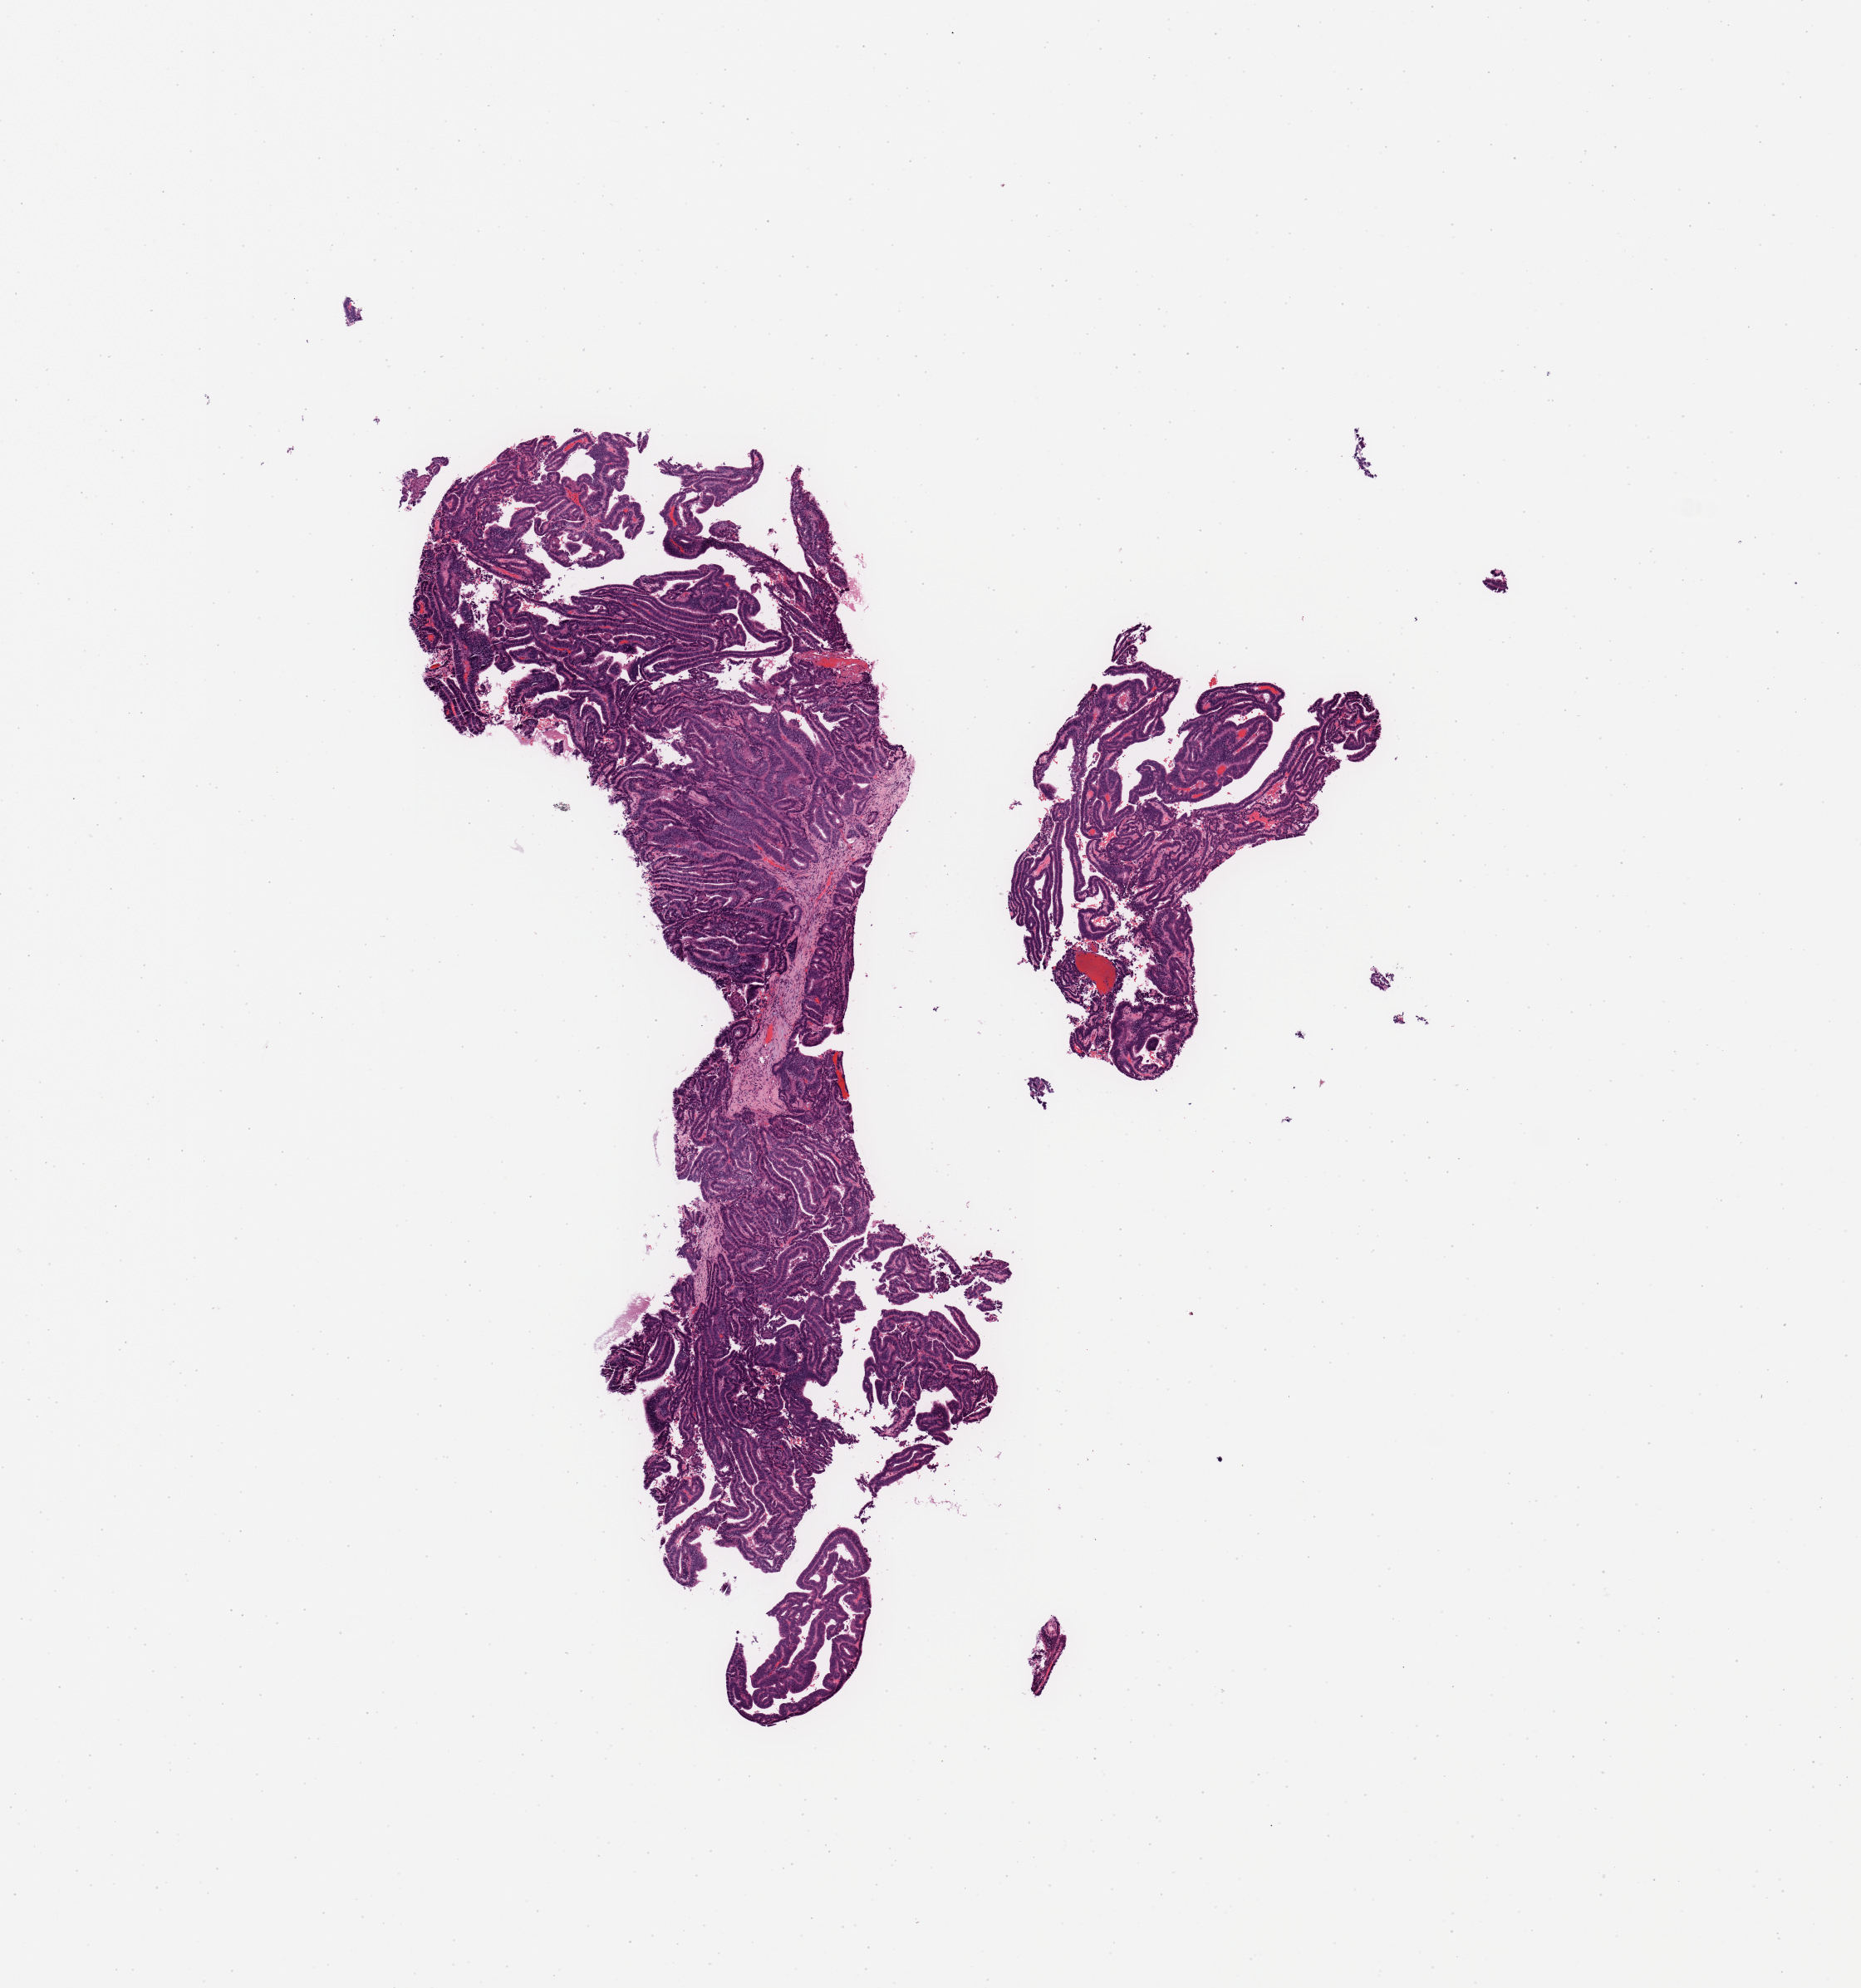
H&E whole-slide image, a low-resolution overview of the entire scanned area, about 8.9 x 9.5 mm (from a 20x scan), tumour tissue sample, uterus. 62-year-old female patient. Histologic grade: G1 (well differentiated).
• diagnosis: Endometrioid adenocarcinoma, NOS
• AJCC pathologic stage: I